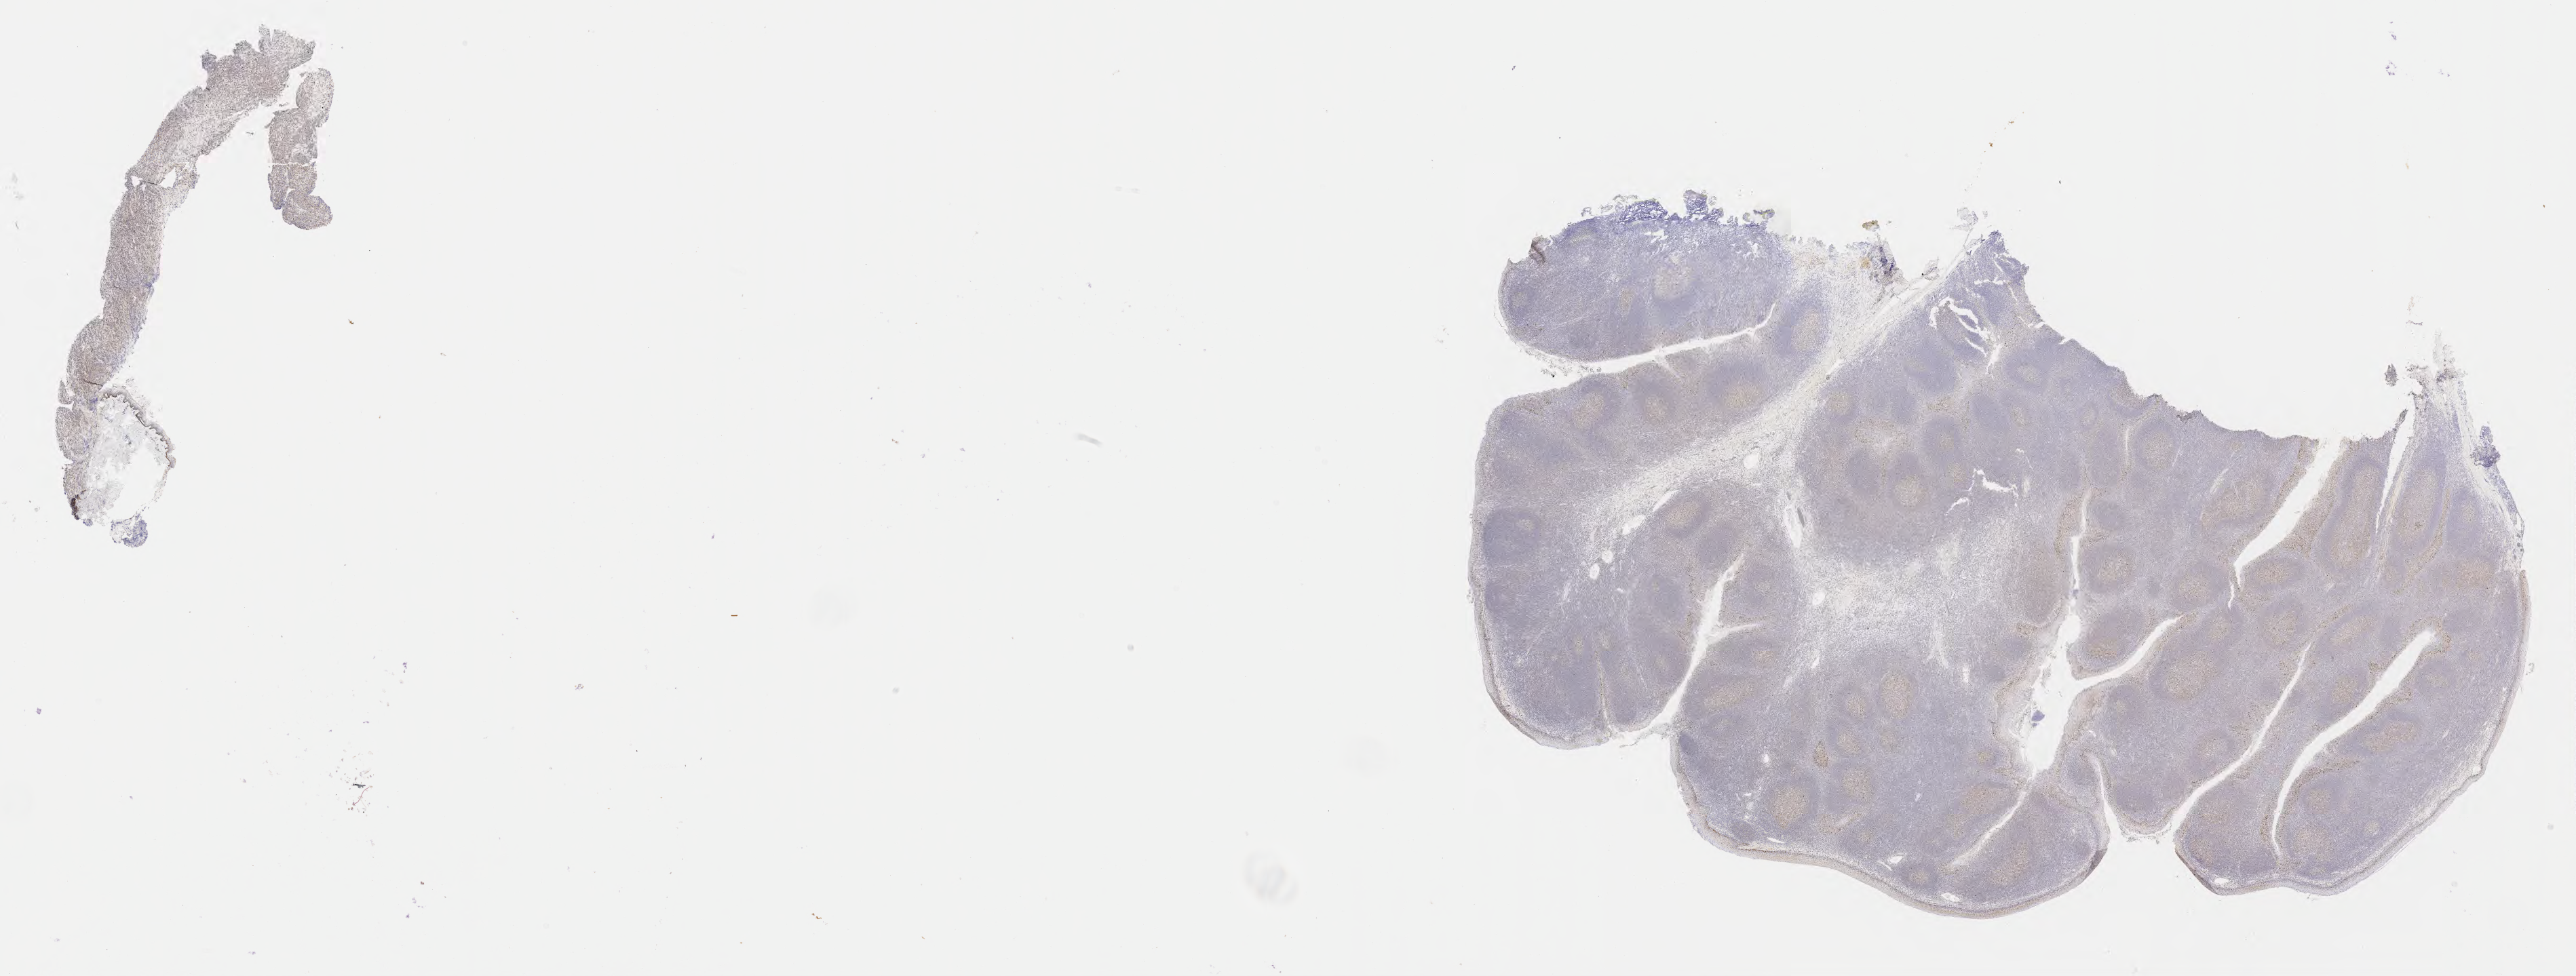
IHC for p53, whole-slide image — a low-resolution overview of the entire scanned area, about 30.7 x 11.6 mm; specimen: tumor tissue. Female patient, aged 43.
Histologic diagnosis: Diffuse large B-cell lymphoma, NOS.